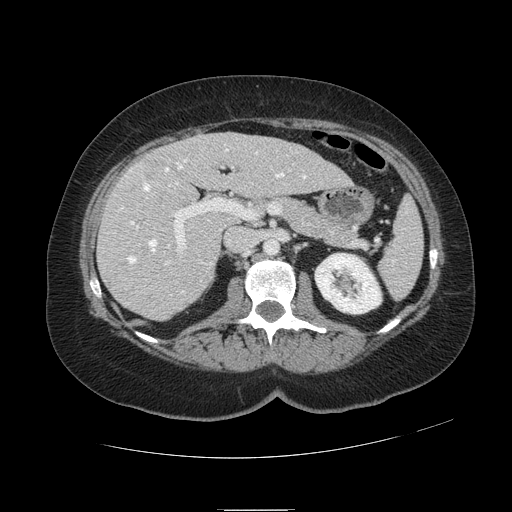
Contrast-enhanced abdominal CT, one axial slice. Position 54 of 121 along the scan axis. Intravenous contrast given. Soft-tissue window (W 400 / L 40 HU). 2.5 mm slice thickness. 512 × 512 image matrix, field of view 400 × 400 mm. Female patient, age 52 years. From the clinical record (not read from this slice): diagnosis: colorectal cancer liver metastases, imaged before liver resection; multiple liver metastases: yes; largest metastasis: 6.3 cm; disease in both lobes: no.
Structures marked on this image (expert manual segmentation):
- hepatic veins: bounding box (x1, y1, x2, y2) in pixels: (121, 149, 306, 293)
- liver: (99, 134, 349, 319)
- planned liver remnant (the part of the liver to remain after resection): (169, 134, 349, 197)
- portal vein (with intrahepatic branches): (131, 169, 291, 264)